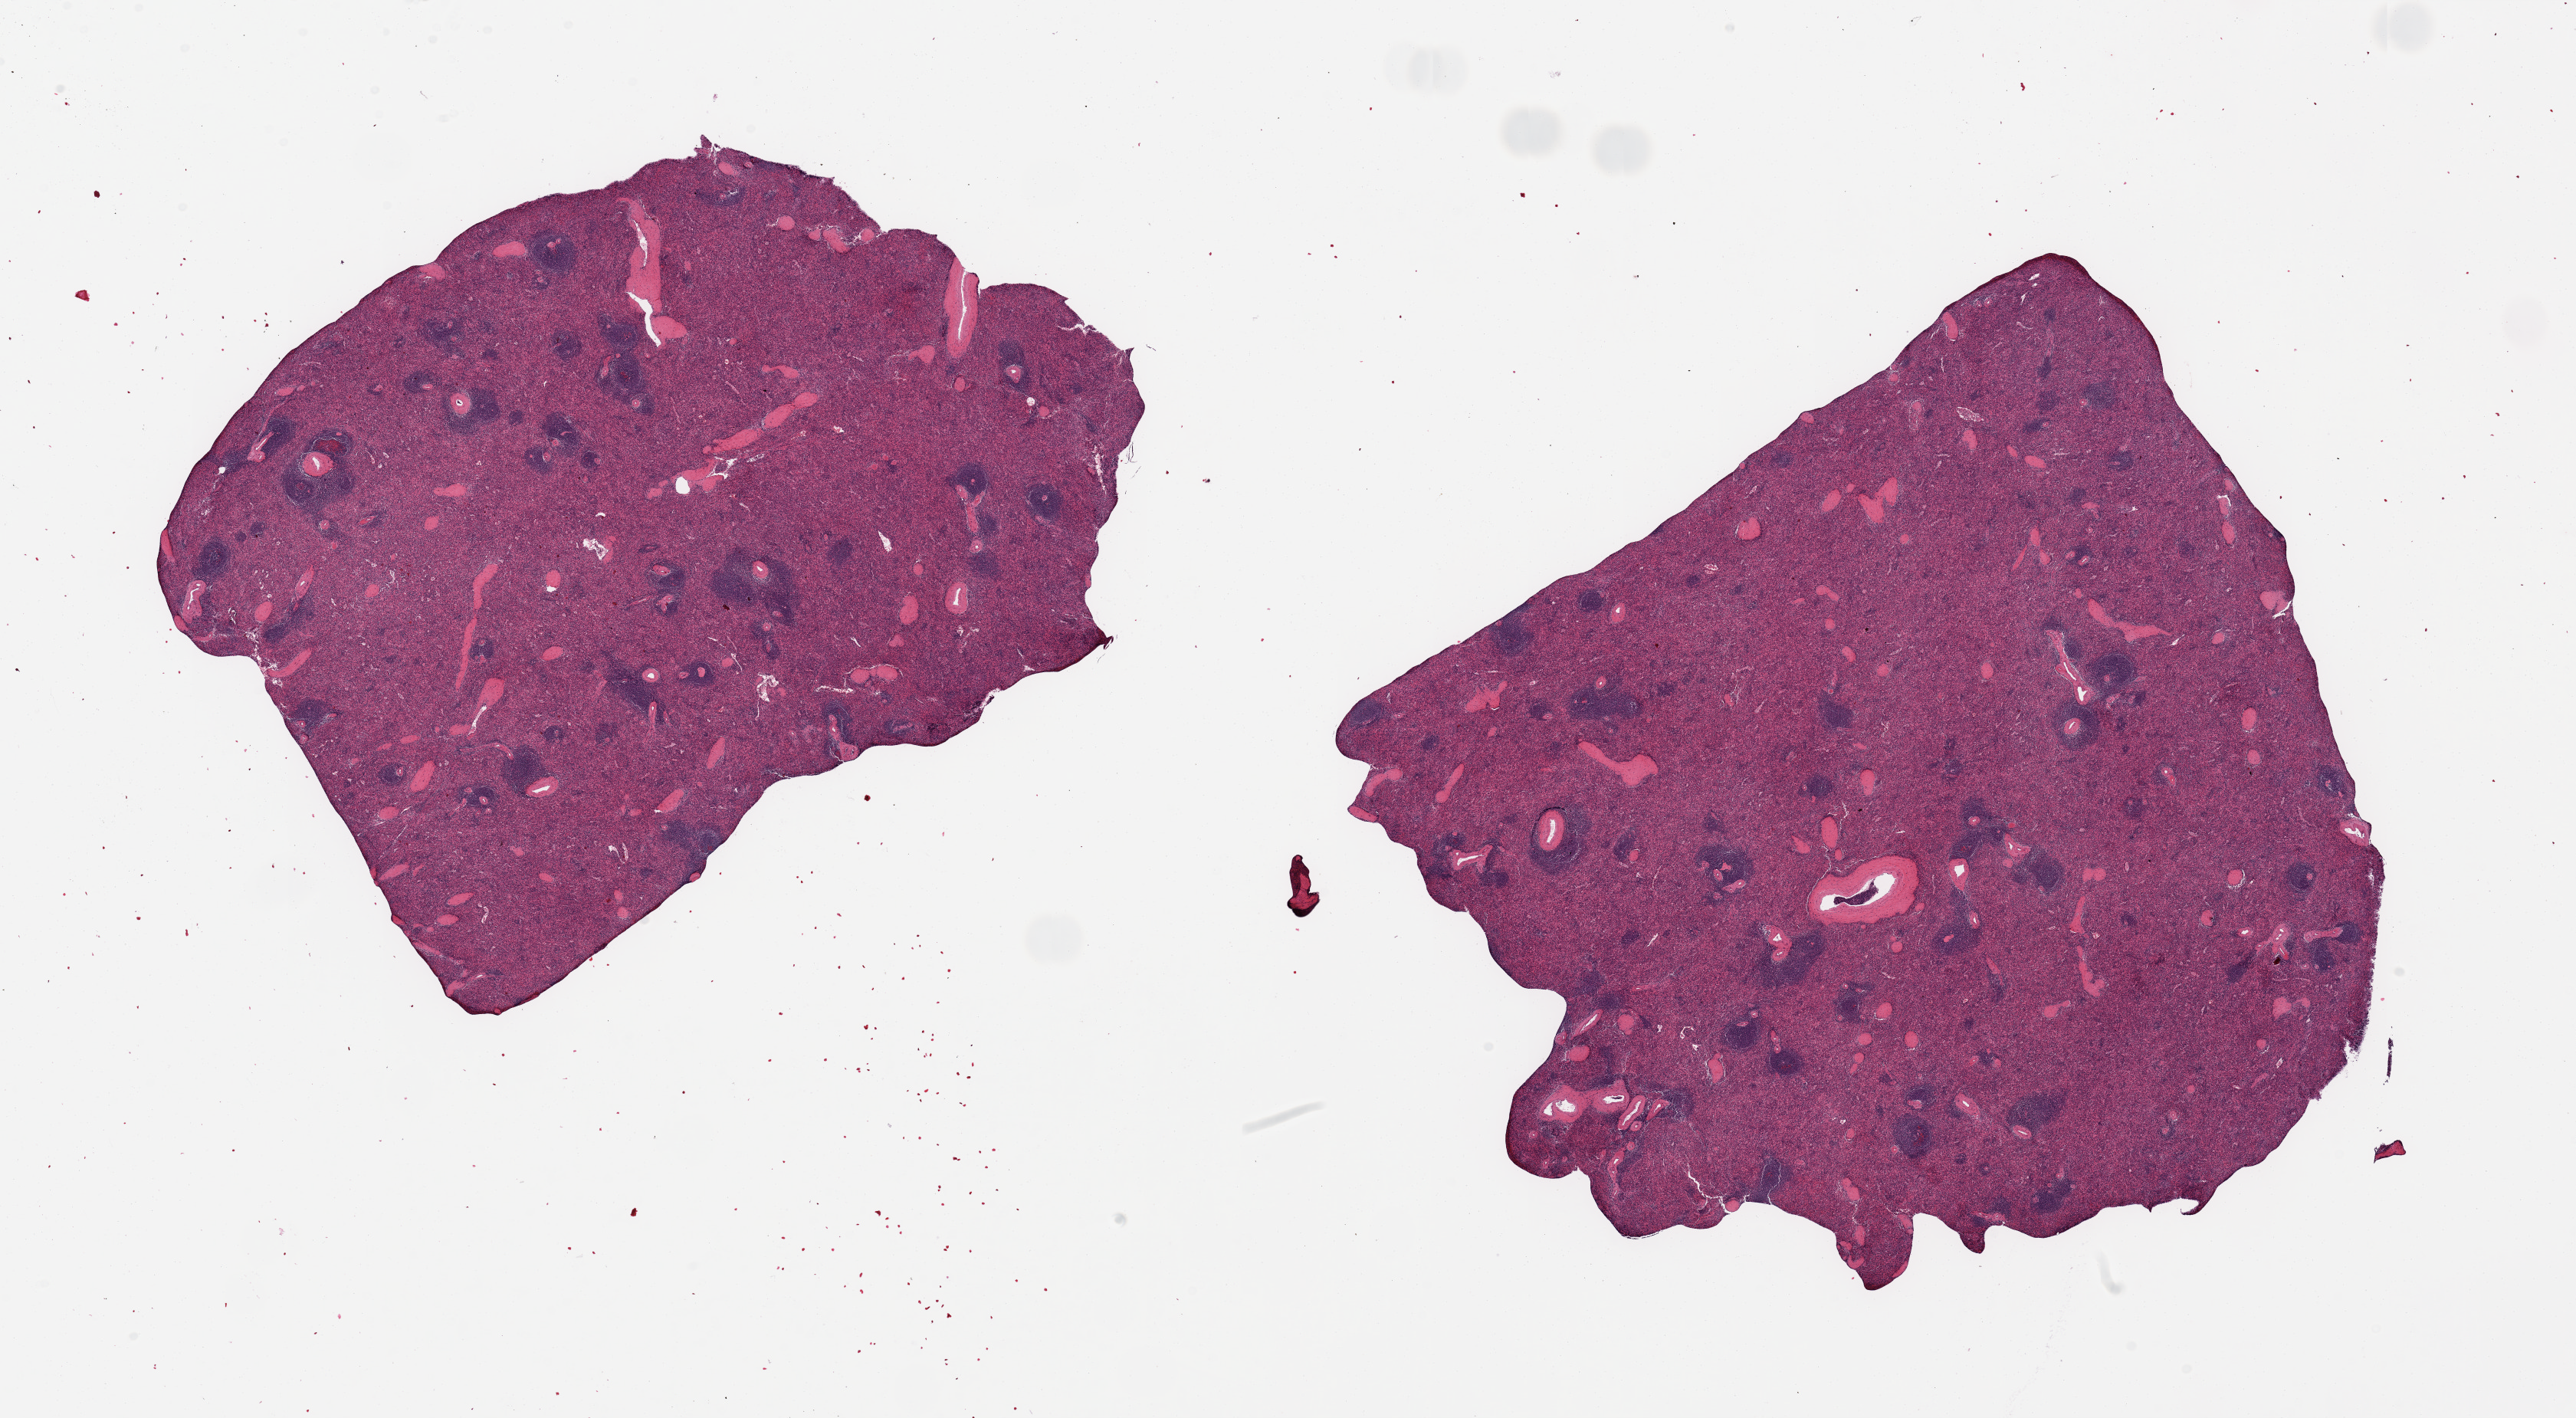
Digitized hematoxylin and eosin (H&E)-stained section — whole scanned area (about 26.6 x 14.6 mm) shown as a low-resolution overview, PAXgene-fixed paraffin-embedded (PFPE) section, target tissue: spleen, donor tissue sample.
Reviewer comment on this tissue sample: 2 pieces; not congested.